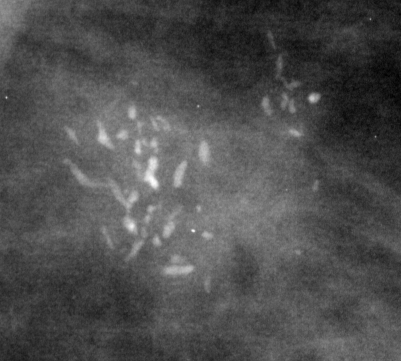
Region of interest cut from a scanned film mammogram (one marked finding), right breast, MLO view, BI-RADS breast density category 3 (scale 1–4).
- Marked abnormality: calcifications, morphology fine linear branching, distribution clustered; BI-RADS assessment category 5; subtlety rating 5 on a 1 (subtle) to 5 (obvious) scale; pathology (as recorded): malignant.